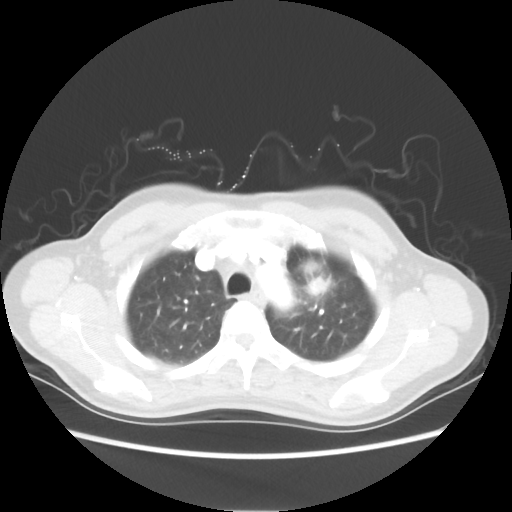
Chest CT, one axial slice. Position 43 of 54 along the scan axis. Reconstruction kernel STANDARD. Lung window (W 1500 / L -600 HU). 512 × 512 image matrix. Patient: female, 53 years. Case-level facts recorded for this patient, not image findings: clinical TNM (as recorded): T1c N0 M0.
Structures marked on this image (bounding box drawn by a radiologist):
- lung tumour (recorded histology: adenocarcinoma): bounding box [x1, y1, x2, y2] px = [297, 256, 334, 303]
- lung tumour (recorded histology: adenocarcinoma): [306, 274, 332, 303]